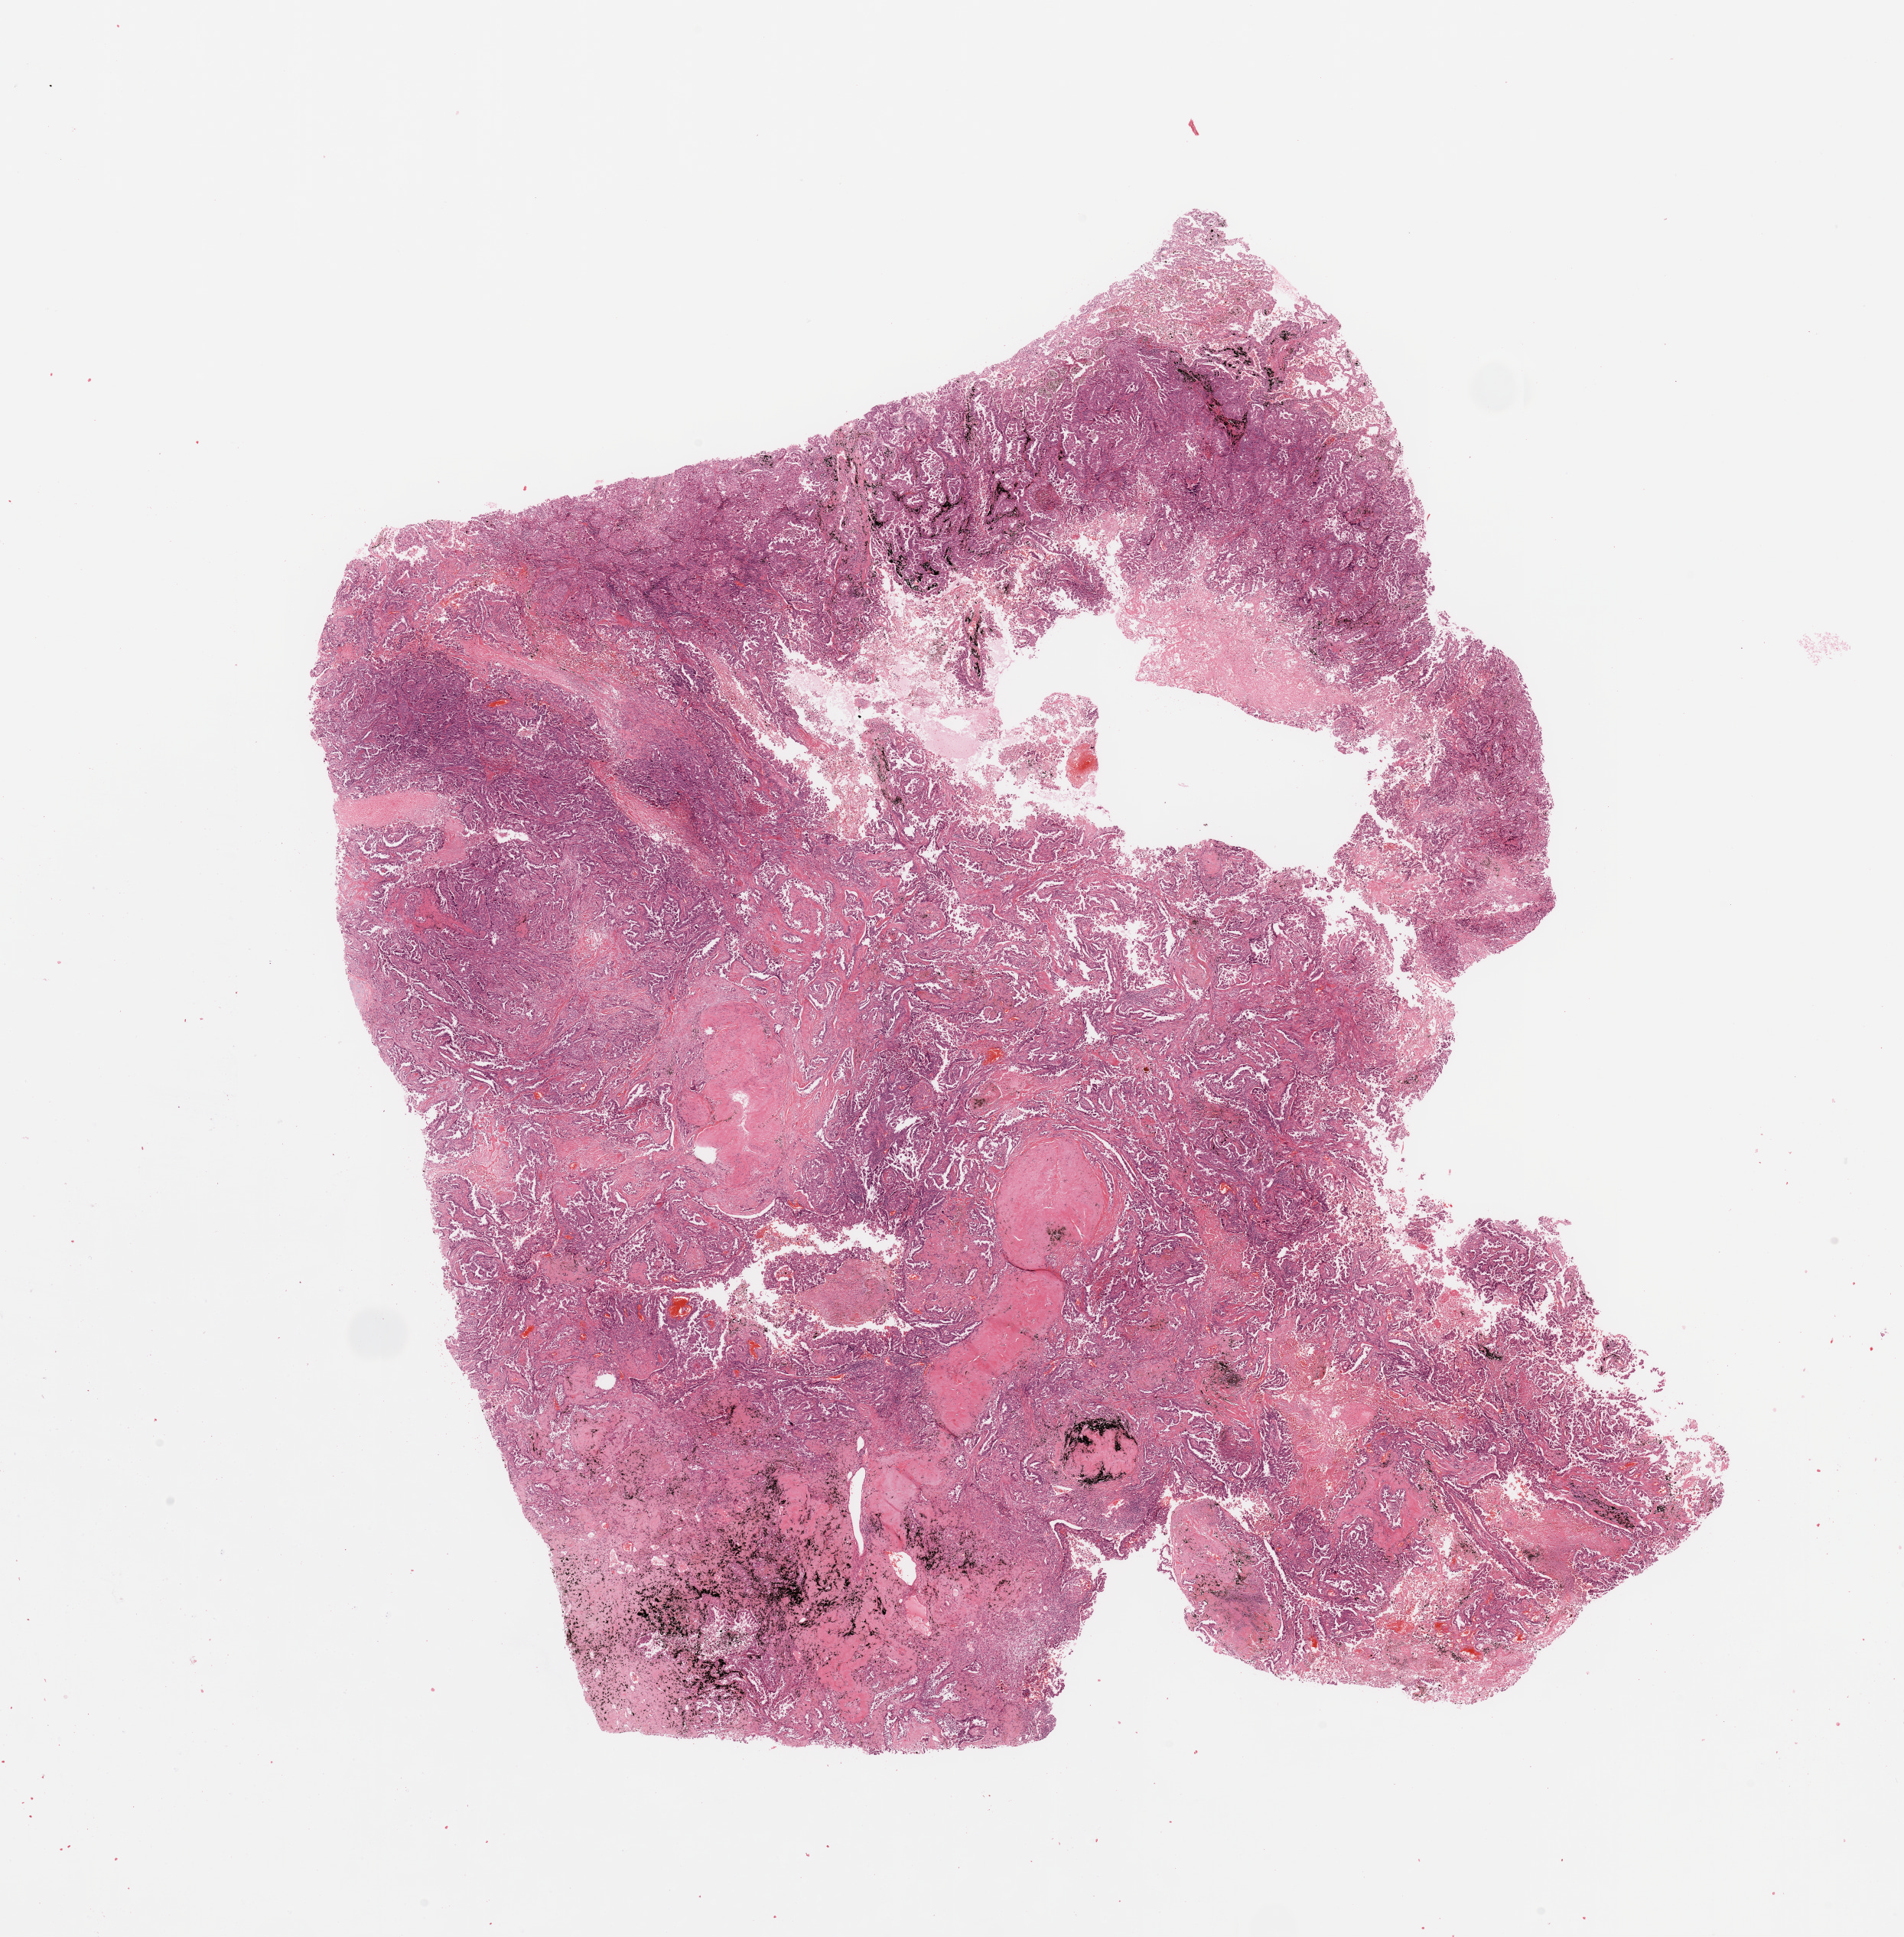
Digitized H&E tissue section (whole slide) — whole scanned area (about 19.7 x 20.0 mm, acquisition: 20x scan) shown as a low-resolution overview, tumour tissue sample, sampled site: lung. 56-year-old male patient. Histologic grade: G2 (moderately differentiated). Composition of this section per pathologist review: tumour nuclei 75%, necrosis 10%.
Histologic diagnosis: Adenocarcinoma, NOS. AJCC pathologic stage: IB.